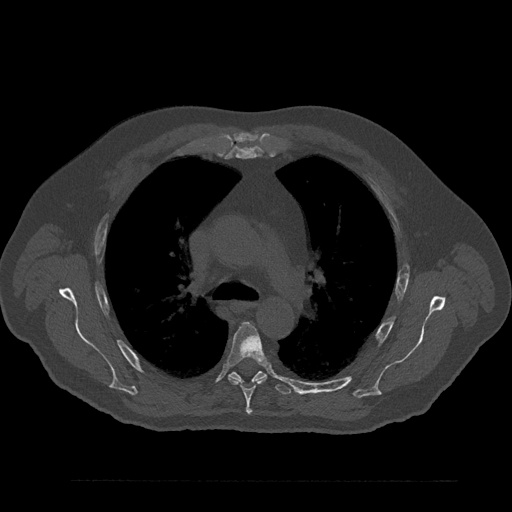
CT including the spine, one axial slice; position 589 of 797 along the scan axis; 120 kVp; bone window (W 1800 / L 400 HU); 0.5 mm slice thickness; 512 × 512 image matrix, field of view 430 × 430 mm. Patient: male, 61 years. Case-level facts recorded for this patient, not image findings: primary cancer: prostate.
Structures marked on this image (semi-automatically segmented with operator editing):
- T5 vertebra: bounding box (x1, y1, x2, y2) in pixels: (226, 322, 267, 415)
- T6 vertebra: (228, 364, 291, 395)